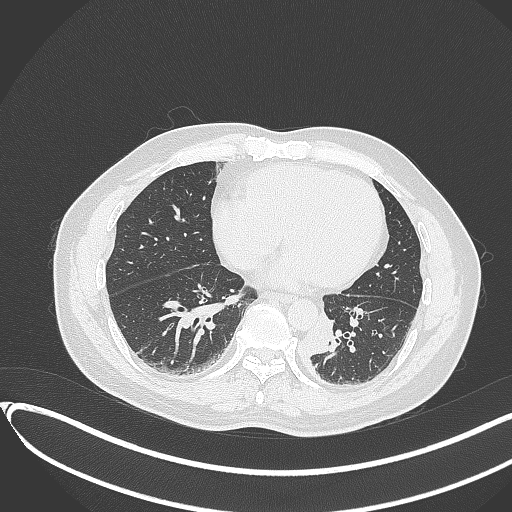
Chest CT, one axial slice. Position 119 of 417 along the scan axis. Lung window (W 1500 / L -600 HU). 512 × 512 image matrix, field of view 400 × 400 mm. Patient: male, 54 years. From the clinical record (not read from this slice): clinical TNM (as recorded): T3 N0 M0.
Outlined on this slice (bounding box drawn by a radiologist):
- lung tumour (recorded histology: squamous cell carcinoma): bounding box [x1, y1, x2, y2] px = [304, 307, 338, 359]